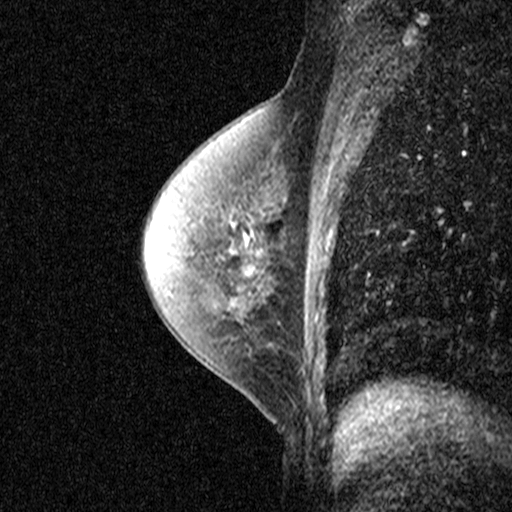
Breast MRI (dynamic contrast-enhanced), one sagittal slice; dynamic contrast-enhanced study with each time point stored as its own series, time point 2 of 3 at this slice position (early post-contrast, ordered by acquisition time); 1.5 T; TE 4.5 ms, TR 11 ms; 3 mm slice thickness; 512 × 512 image matrix, field of view 200 × 200 mm. Patient: female, 55 years. From the clinical record (not read from this slice): setting: breast cancer imaged before/during neoadjuvant chemotherapy; receptor status: HR-positive, HER2-negative.
Annotated regions visible in this slice (semi-automatically segmented with operator editing):
- analysis volume of interest (the breast-tissue region the enhancement analysis was run in; not a lesion): box from (x=194, y=202) to (x=279, y=277) px
- tumour enhancement mask (voxels above the 90 % enhancement threshold inside the analysis volume of interest): (x=243, y=232)–(x=248, y=246)